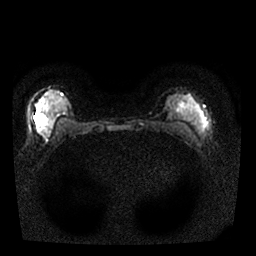
Breast MRI, one axial slice; slice 13 of 25 in the series (ordered by position); diffusion-weighted series; image 2 of 4 stored at this slice position (different b-values; order by instance number); 1.5 T; 256 × 256 image matrix, field of view 310 × 310 mm. Female patient.
Annotated regions visible in this slice (manually delineated by an expert):
- tumour on diffusion-weighted imaging: bounding box <39,124,48,135> (left, top, right, bottom; pixels)